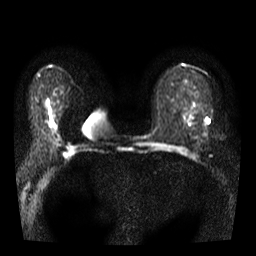
Breast MRI, one axial slice. Slice 20 of 38 in the series (ordered by position). Diffusion-weighted series; image 2 of 4 stored at this slice position (different b-values; order by instance number). 3 T. 5 mm slice thickness. 256 × 256 image matrix. Female patient.
Annotated regions visible in this slice (outlined manually by an expert reader):
- tumour on diffusion-weighted imaging: bounding box [x1, y1, x2, y2] px = [206, 118, 210, 124]